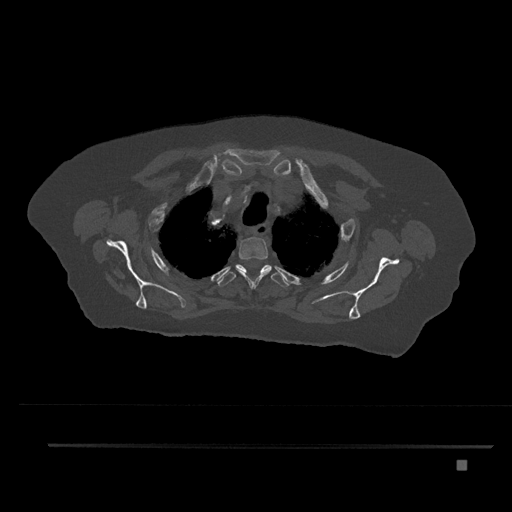
CT including the spine, one axial slice; 120 kVp; bone window (W 1800 / L 400 HU); 512 × 512 image matrix. Patient: female, 76 years. From the clinical record (not read from this slice): primary cancer: lung.
Outlined on this slice (semi-automatically segmented with operator editing):
- T2 vertebra: box from (x=235, y=231) to (x=271, y=289) px
- T3 vertebra: (x=218, y=264)–(x=289, y=288)